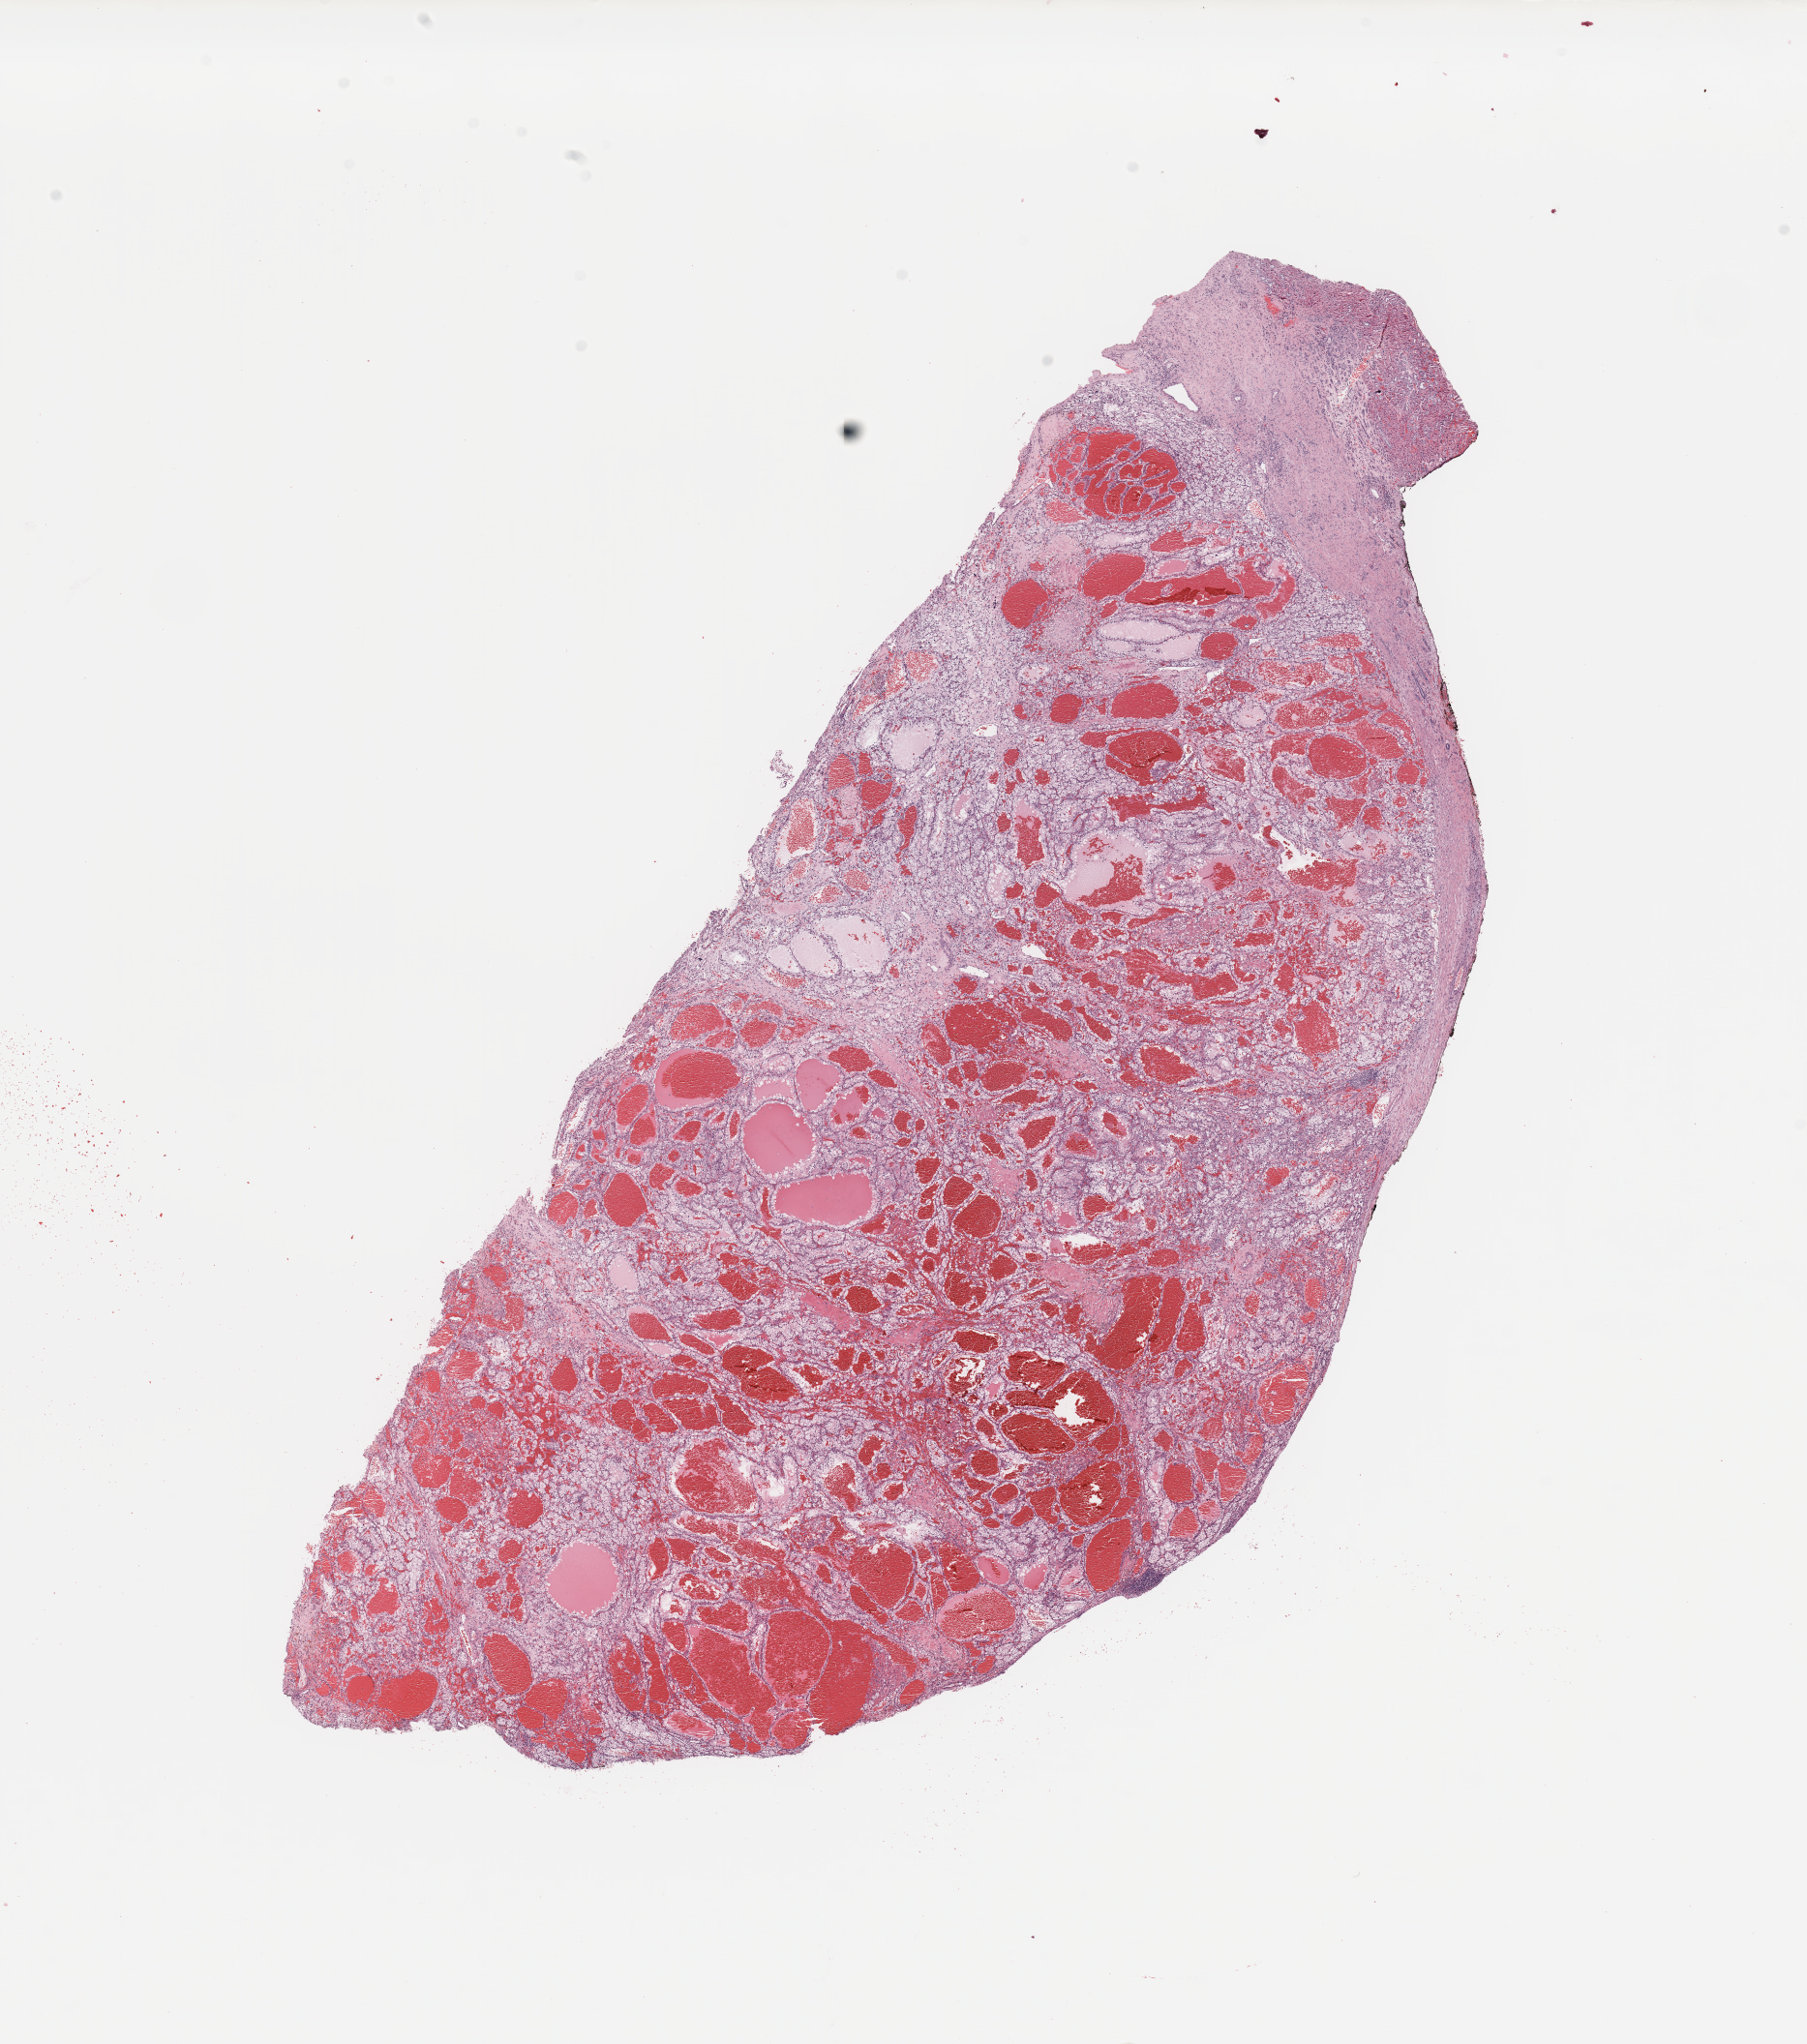
Digitized H&E-stained tissue section (whole slide), whole scanned area (about 14.8 x 16.7 mm, from a 20x scan) shown as a low-resolution overview. Tumour tissue sample, sampled site: kidney. Female, 54 y/o. Histologic grade: G3 (poorly differentiated). Slide review estimates, as recorded: tumour nuclei 80%, necrosis 5%.
Histologic diagnosis: Renal cell carcinoma, NOS. AJCC pathologic stage: I. Primary tumour site (as recorded): lower pole.